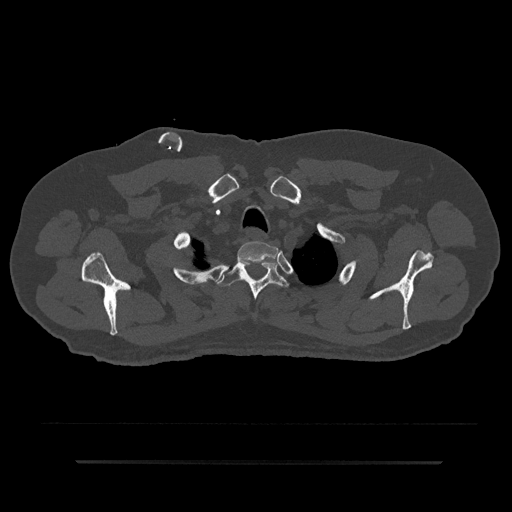
CT including the spine, one axial slice; slice 709 of 797 in the series (ordered by position); 120 kVp; bone window (W 1800 / L 400 HU); 512 × 512 image matrix, field of view 464 × 464 mm. Male patient, age 59 years. From the clinical record (not read from this slice): primary cancer: bile ducts; vertebrae with lytic lesions (as recorded): T10.
Structures marked on this image (semi-automatic segmentation, software-assisted and operator-edited):
- T1 vertebra: bounding box (x1, y1, x2, y2) in pixels: (237, 241, 278, 264)
- T2 vertebra: (217, 262, 289, 300)